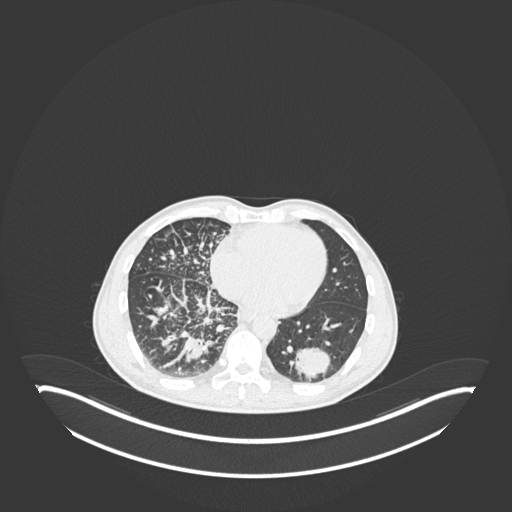
Chest CT, one axial slice. Position 78 of 237 along the scan axis. Reconstruction kernel B30f. 120 kVp. Lung window (W 1500 / L -600 HU). 1 mm slice thickness. 512 × 512 image matrix, field of view 500 × 500 mm. Male patient, age 49 years. Case-level facts recorded for this patient, not image findings: clinical TNM (as recorded): T2b N1 M0.
Outlined on this slice (rectangle marked by the reading radiologist):
- lung tumour (recorded histology: adenocarcinoma): bounding box <289,341,334,383> (left, top, right, bottom; pixels)